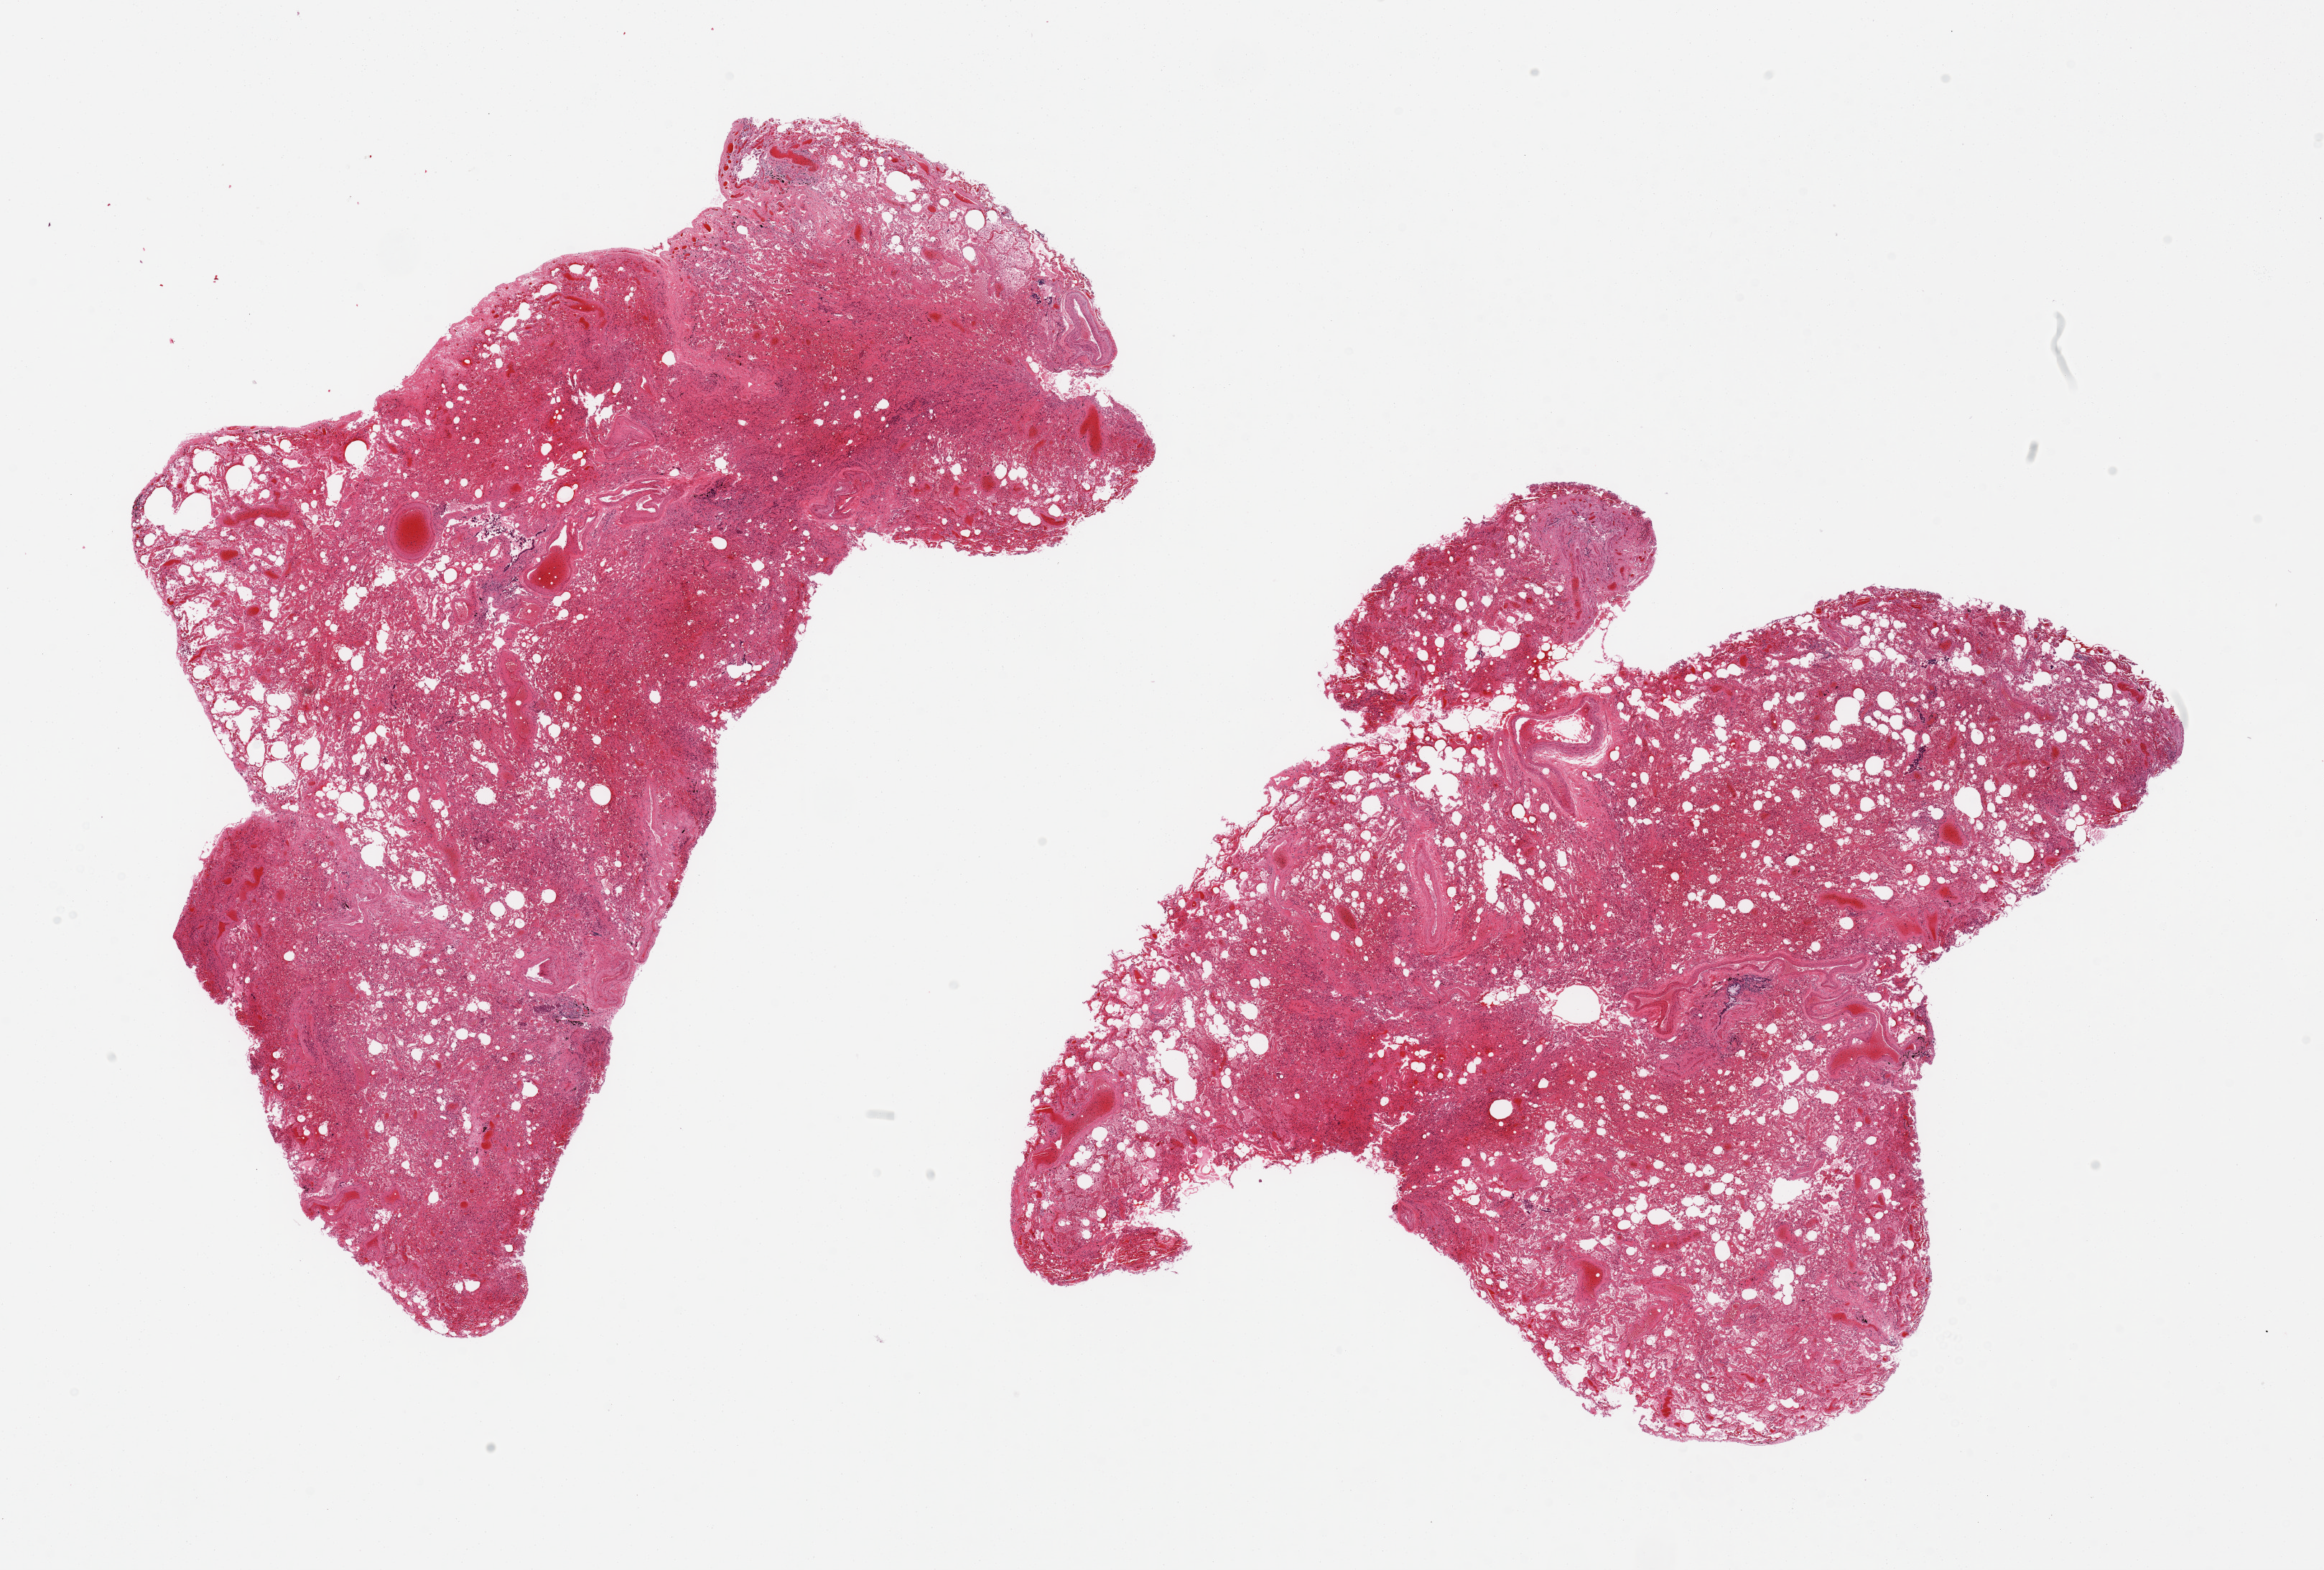
Haematoxylin and eosin whole-slide image, a low-resolution overview of the entire scanned area, about 25.6 x 17.3 mm; PAXgene-fixed, paraffin-embedded tissue; target tissue: lung; tissue donor sample.
Pathologist's review note for this sample: 2 pieces, congestion, fibrosis, edema, and atelectasis.